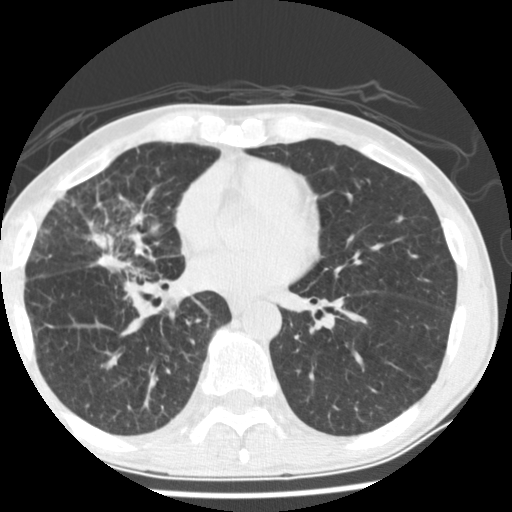
Low-dose screening chest CT, one axial slice. Position 74 of 162 along the scan axis. 120 kVp. Lung window (W 1500 / L -600 HU). 2.5 mm slice thickness. 512 × 512 image matrix.
Outlined on this slice (manually delineated by an expert):
- lesion 1 (tumor, middle lobe of right lung): bounding box (x1, y1, x2, y2) in pixels: (74, 235, 118, 270)